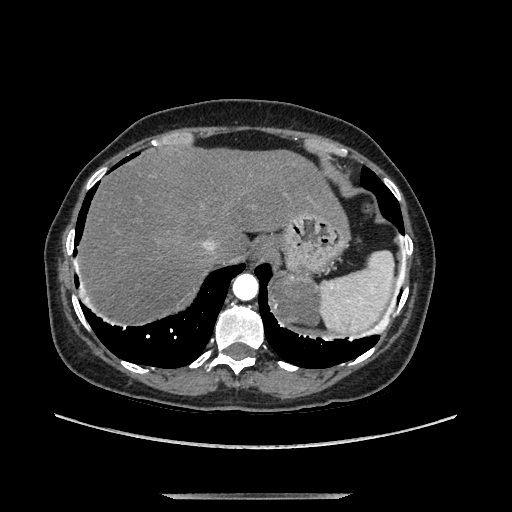
Contrast-enhanced abdominal CT, one axial slice. Position 115 of 169 along the scan axis. Soft-tissue window (W 400 / L 40 HU). 1.25 mm slice thickness. 512 × 512 image matrix. Female patient. From the clinical record (not read from this slice): diagnosis: adrenocortical carcinoma; tumour side: left adrenal; tumour size at pathology: 9 cm; Ki-67 index: 2 %; stage (as recorded): 3.
Structures marked on this image (semi-automatically segmented with operator editing):
- mass: bounding box [x1, y1, x2, y2] px = [273, 278, 319, 325]